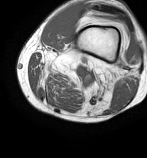
MRI of an extremity soft-tissue mass, one axial slice; position 15 of 86 along the scan axis; MR volume resampled by the dataset authors to the PET/CT grid (not the native acquisition matrix); 3.27 mm slice thickness; 147 × 158 image matrix, field of view 144 × 154 mm. Male patient. From the clinical record (not read from this slice): histological type: undifferentiated pleomorphic liposarcoma; grade: high; site of the primary tumour: left thigh.
Annotated regions visible in this slice (expert contour drawn on MRI and transferred to this co-registered scan by the dataset authors):
- gross tumour volume including surrounding oedema: bounding box (x1, y1, x2, y2) in pixels: (39, 60, 113, 89)